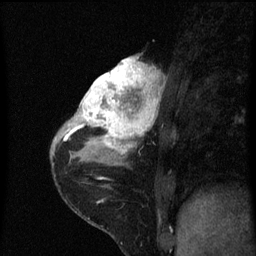
Breast MRI (dynamic contrast-enhanced), one sagittal slice; slice 25 of 60 in the series (ordered by position); dynamic contrast-enhanced series, image 2 of 3 at this slice position (ordered by acquisition); 1.5 T; TE 4.2 ms, TR 8 ms; 2 mm slice thickness; 256 × 256 image matrix, field of view 180 × 180 mm. Patient: female, 38 years.
Outlined on this slice (semi-automatically segmented with operator editing):
- analysis volume of interest (the breast-tissue region the enhancement analysis was run in; not a lesion): box from (x=80, y=56) to (x=165, y=151) px
- tumour enhancement mask (voxels above the 70 % enhancement threshold inside the analysis volume of interest): (x=80, y=56)–(x=161, y=151)